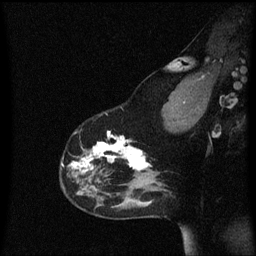
Breast MRI (dynamic contrast-enhanced), one sagittal slice. Position 44 of 60 along the scan axis. Dynamic contrast-enhanced series, image 2 of 3 at this slice position (ordered by acquisition). 1.5 T. TE 4.2 ms, TR 8.4 ms. 2 mm slice thickness. 256 × 256 image matrix. Patient: female, 33 years.
Outlined on this slice (semi-automatically segmented with operator editing):
- analysis volume of interest (the breast-tissue region the enhancement analysis was run in; not a lesion): bounding box <61,116,152,191> (left, top, right, bottom; pixels)
- tumour enhancement mask (voxels above the 70 % enhancement threshold inside the analysis volume of interest): <62,132,150,173>